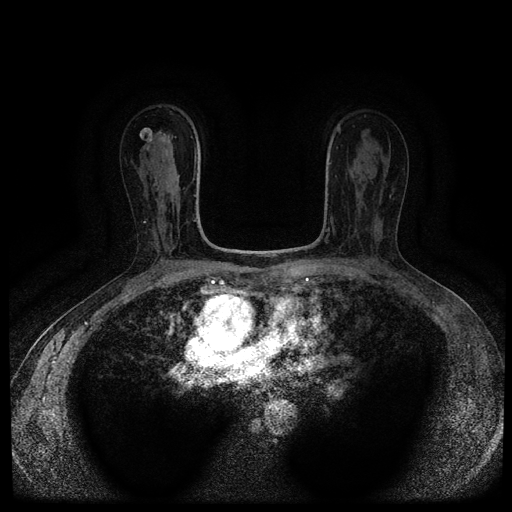
Breast MRI (dynamic contrast-enhanced, multi-phase), one axial slice. Slice 61 of 116 in the series (ordered by position). Dynamic contrast-enhanced series, time point 2 of 5 at this slice position (early post-contrast). 1.5 T. TE 2.7 ms, TR 5.4 ms. 512 × 512 image matrix, field of view 330 × 330 mm. Patient: female, 63 years.
Outlined on this slice (semi-automatic segmentation, software-assisted and operator-edited):
- breast lesion (labelled benign in the annotation): bounding box <139,128,153,142> (left, top, right, bottom; pixels)